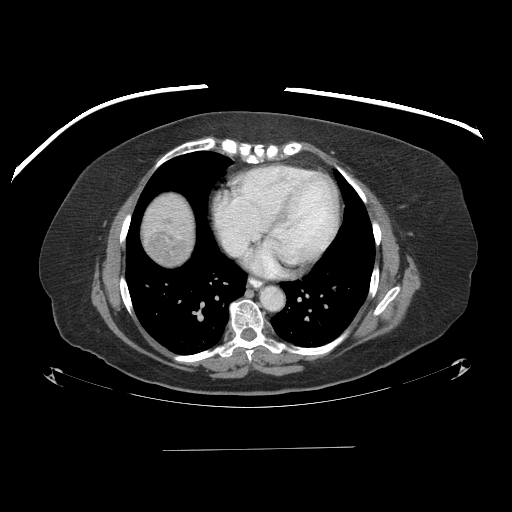
Contrast-enhanced abdominal CT (liver protocol), one axial slice. Position 87 of 103 along the scan axis. 120 kVp. One of 2 acquisitions stored at this slice position. Soft-tissue window (W 400 / L 40 HU). 512 × 512 image matrix. From the clinical record (not read from this slice): diagnosis: hepatocellular carcinoma (patient treated with transarterial chemoembolisation; whether this scan precedes or follows treatment is not stated here); TNM stage (as recorded): Stage-IIIA; Child-Pugh class: A; tumour differentiation: poorly differentiated; tumour nodularity: multinodular.
Outlined on this slice (semi-automatic segmentation, software-assisted and operator-edited):
- liver parenchyma outside the tumour (the mass and vessels are separate outlines, so this box may not span the whole liver): box from (x=142, y=192) to (x=194, y=266) px
- mass: (x=147, y=230)–(x=184, y=262)